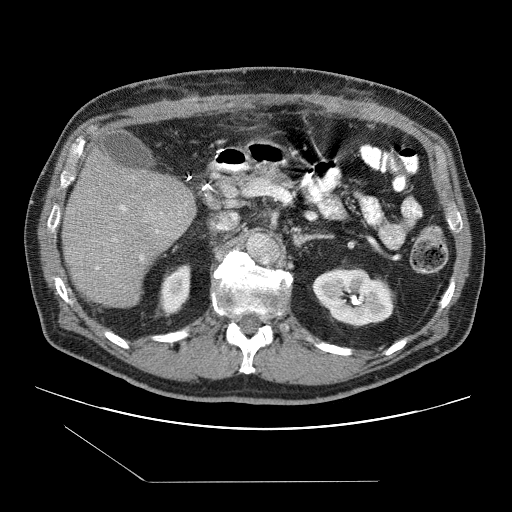
Contrast-enhanced abdominal CT (liver protocol), one axial slice; position 46 of 109 along the scan axis; reconstruction kernel STANDARD; 120 kVp; one of 2 acquisitions stored at this slice position; soft-tissue window (W 400 / L 40 HU); 512 × 512 image matrix, field of view 400 × 400 mm. From the clinical record (not read from this slice): diagnosis: hepatocellular carcinoma (patient treated with transarterial chemoembolisation; whether this scan precedes or follows treatment is not stated here); TNM stage (as recorded): Stage-IIIB; Child-Pugh class: A; tumour nodularity: multinodular.
Structures marked on this image (semi-automatic segmentation, software-assisted and operator-edited):
- liver parenchyma outside the tumour (the mass and vessels are separate outlines, so this box may not span the whole liver): bounding box (x1, y1, x2, y2) in pixels: (62, 149, 196, 308)
- liver vessels: (96, 205, 159, 270)